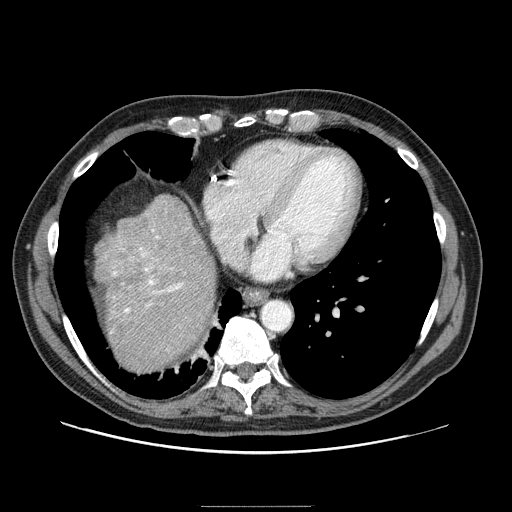
Contrast-enhanced abdominal CT (liver protocol), one axial slice; slice 81 of 99 in the series (ordered by position); reconstruction kernel STANDARD; 100 kVp; one of 2 acquisitions stored at this slice position; soft-tissue window (W 400 / L 40 HU); 512 × 512 image matrix, field of view 400 × 400 mm. Case-level facts recorded for this patient, not image findings: diagnosis: hepatocellular carcinoma (patient treated with transarterial chemoembolisation; whether this scan precedes or follows treatment is not stated here); TNM stage (as recorded): Stage-II.
Outlined on this slice (semi-automatic segmentation, software-assisted and operator-edited):
- liver parenchyma outside the tumour (the mass and vessels are separate outlines, so this box may not span the whole liver): box from (x=98, y=194) to (x=216, y=372) px
- liver vessels: (x=111, y=229)–(x=183, y=333)